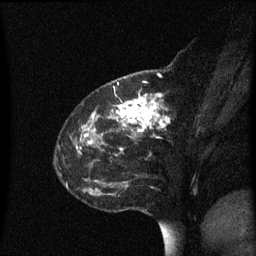
Breast MRI (dynamic contrast-enhanced), one sagittal slice; slice 21 of 60 in the series (ordered by position); dynamic contrast-enhanced series, image 2 of 3 at this slice position (ordered by acquisition); 1.5 T; TE 4.2 ms, TR 8.4 ms; 2 mm slice thickness; 256 × 256 image matrix, field of view 200 × 200 mm. Female patient, age 48 years. From the clinical record (not read from this slice): setting: breast cancer imaged before/during neoadjuvant chemotherapy; receptor status: HR-positive, HER2-negative.
Annotated regions visible in this slice (semi-automatic segmentation, software-assisted and operator-edited):
- analysis volume of interest (the breast-tissue region the enhancement analysis was run in; not a lesion): bounding box [x1, y1, x2, y2] px = [80, 78, 195, 215]
- tumour enhancement mask (voxels above the 70 % enhancement threshold inside the analysis volume of interest): [86, 83, 171, 183]